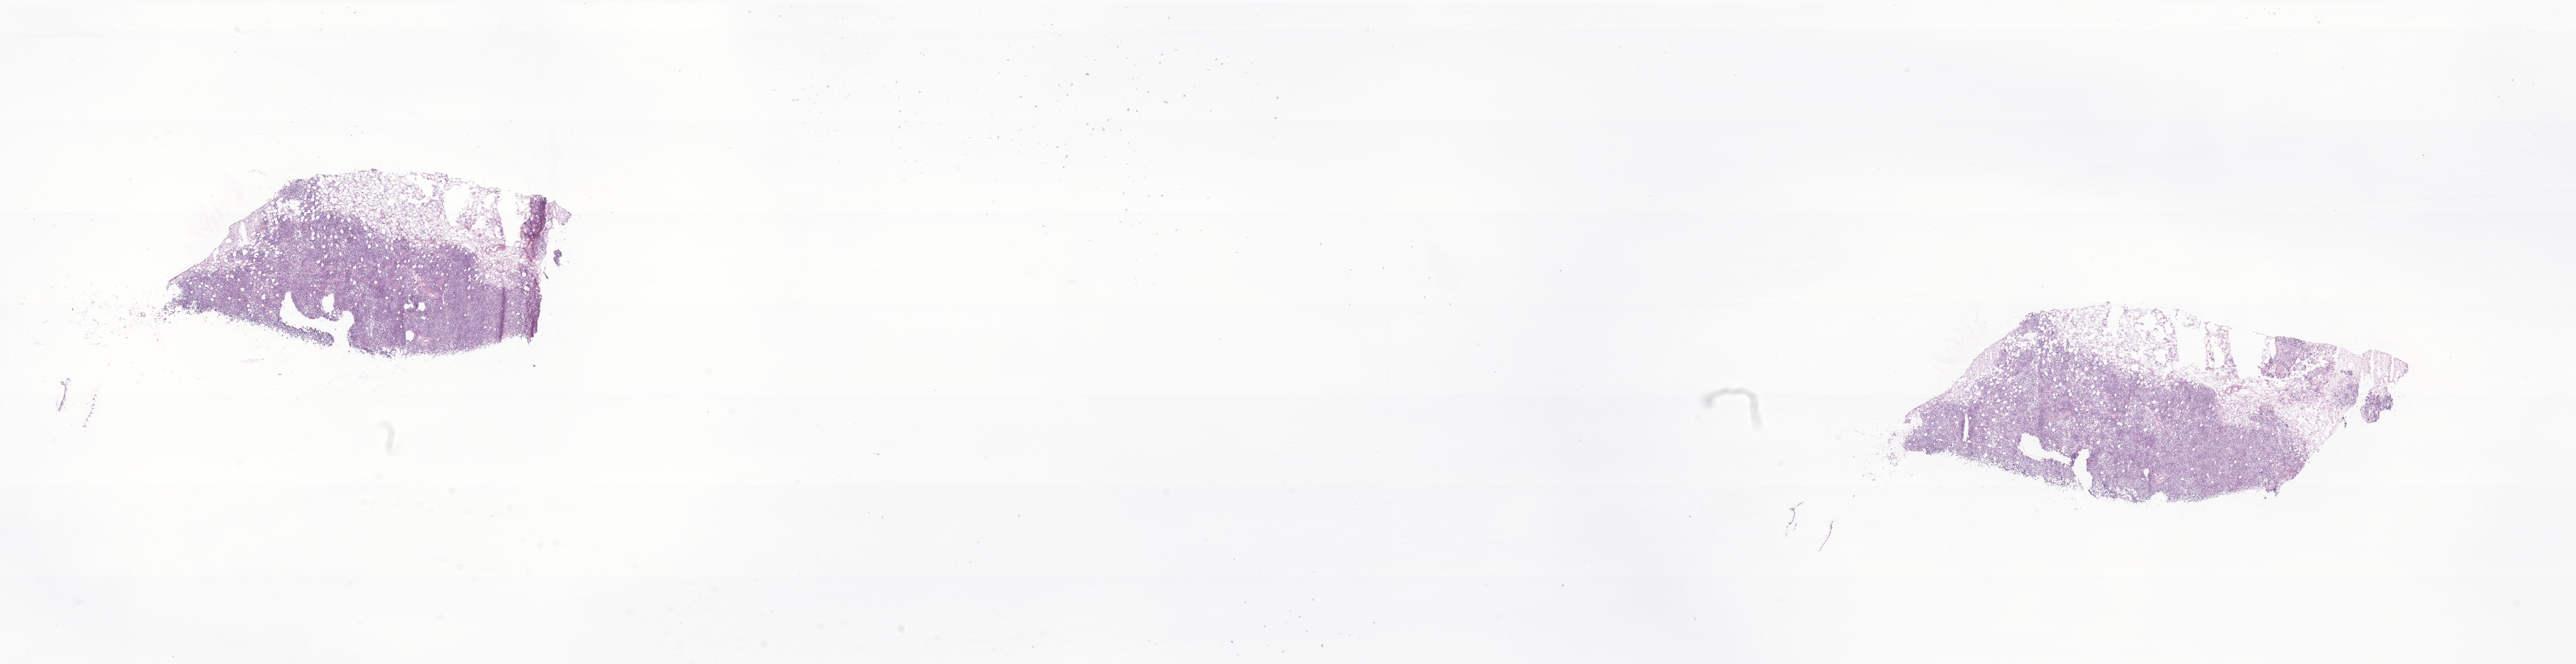
Hematoxylin and eosin (H&E) whole-slide image of tumor tissue from the soft tissue of lower extremity, shown as a low-resolution overview of the whole scanned area (about 30.2 x 7.8 mm), frozen section. Female patient, age 35 months (2 years 11 months).
Tissue or organ of origin (case record): connective, subcutaneous and other soft tissues of lower limb and hip. Recorded diagnosis: Rhabdomyosarcoma, NOS.